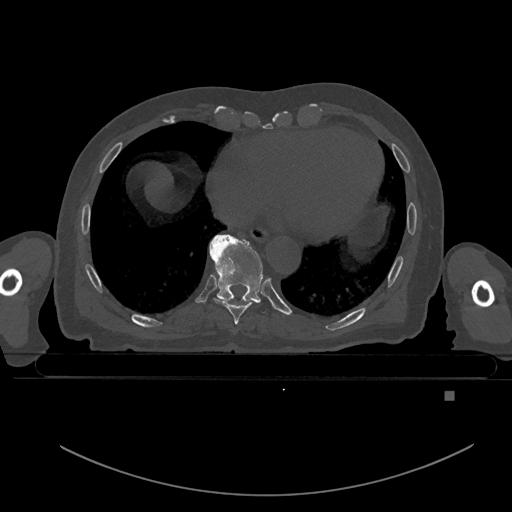
CT including the spine, one axial slice; position 172 of 969 along the scan axis; bone window (W 1800 / L 400 HU); 0.5 mm slice thickness; 512 × 512 image matrix. Male patient, age 82 years. From the clinical record (not read from this slice): primary cancer: prostate.
Structures marked on this image (semi-automatically segmented with operator editing):
- T8 vertebra: box from (x=213, y=297) to (x=253, y=324) px
- T9 vertebra: (x=209, y=234)–(x=267, y=313)